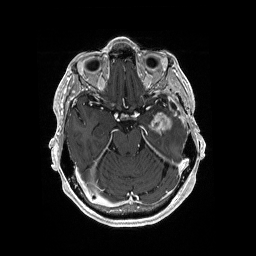
Brain MRI from a brain-tumour surgery series, one axial slice; position 119 of 176 along the scan axis; T1-weighted post-contrast; 1 mm slice thickness; 256 × 256 image matrix. From the clinical record (not read from this slice): histopathology: Glioblastoma; WHO grade: 4.
Structures marked on this image (expert manual segmentation):
- previous resection cavity: bounding box <171,104,176,109> (left, top, right, bottom; pixels)
- tumour: <148,112,174,134>